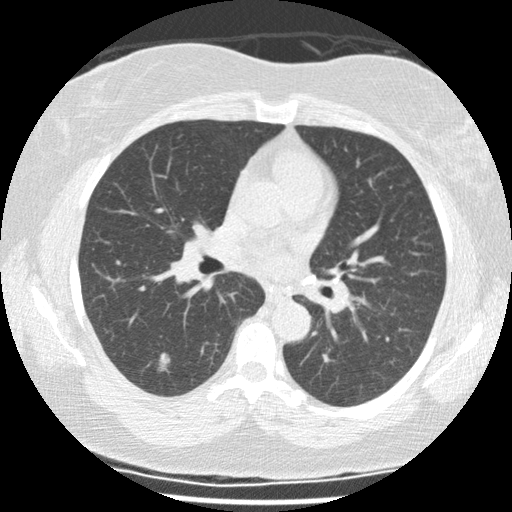
Low-dose screening chest CT, axial slice. Second annual screen. Lung window (W 1500 / L -600 HU). 2.5 mm slice thickness. Standard (soft-tissue) reconstruction kernel (STANDARD). Slice 55 of 117 in the series. 512 × 512 image matrix, field of view 325 × 325 mm. Female participant, aged 65 years at enrolment. Current smoker at enrolment.
Expert reader's lesion annotation, bounding box <140,346,180,383> (left, top, right, bottom; pixels). Screening reader's record for this exam (one nodule recorded; not confirmed to be the boxed lesion): non-calcified nodule or mass ≥4 mm, right lower lobe, 12 × 8 mm, spiculated (stellate) margins, mixed attenuation, pre-existing on the prior screen: yes; interval growth: yes. Official screen result: positive, other. Lung cancer was diagnosed 84 days after this screen: non-small cell carcinoma, right lower lobe, well differentiated (G1), stage IA (AJCC 6th edition), 10 mm at pathology.